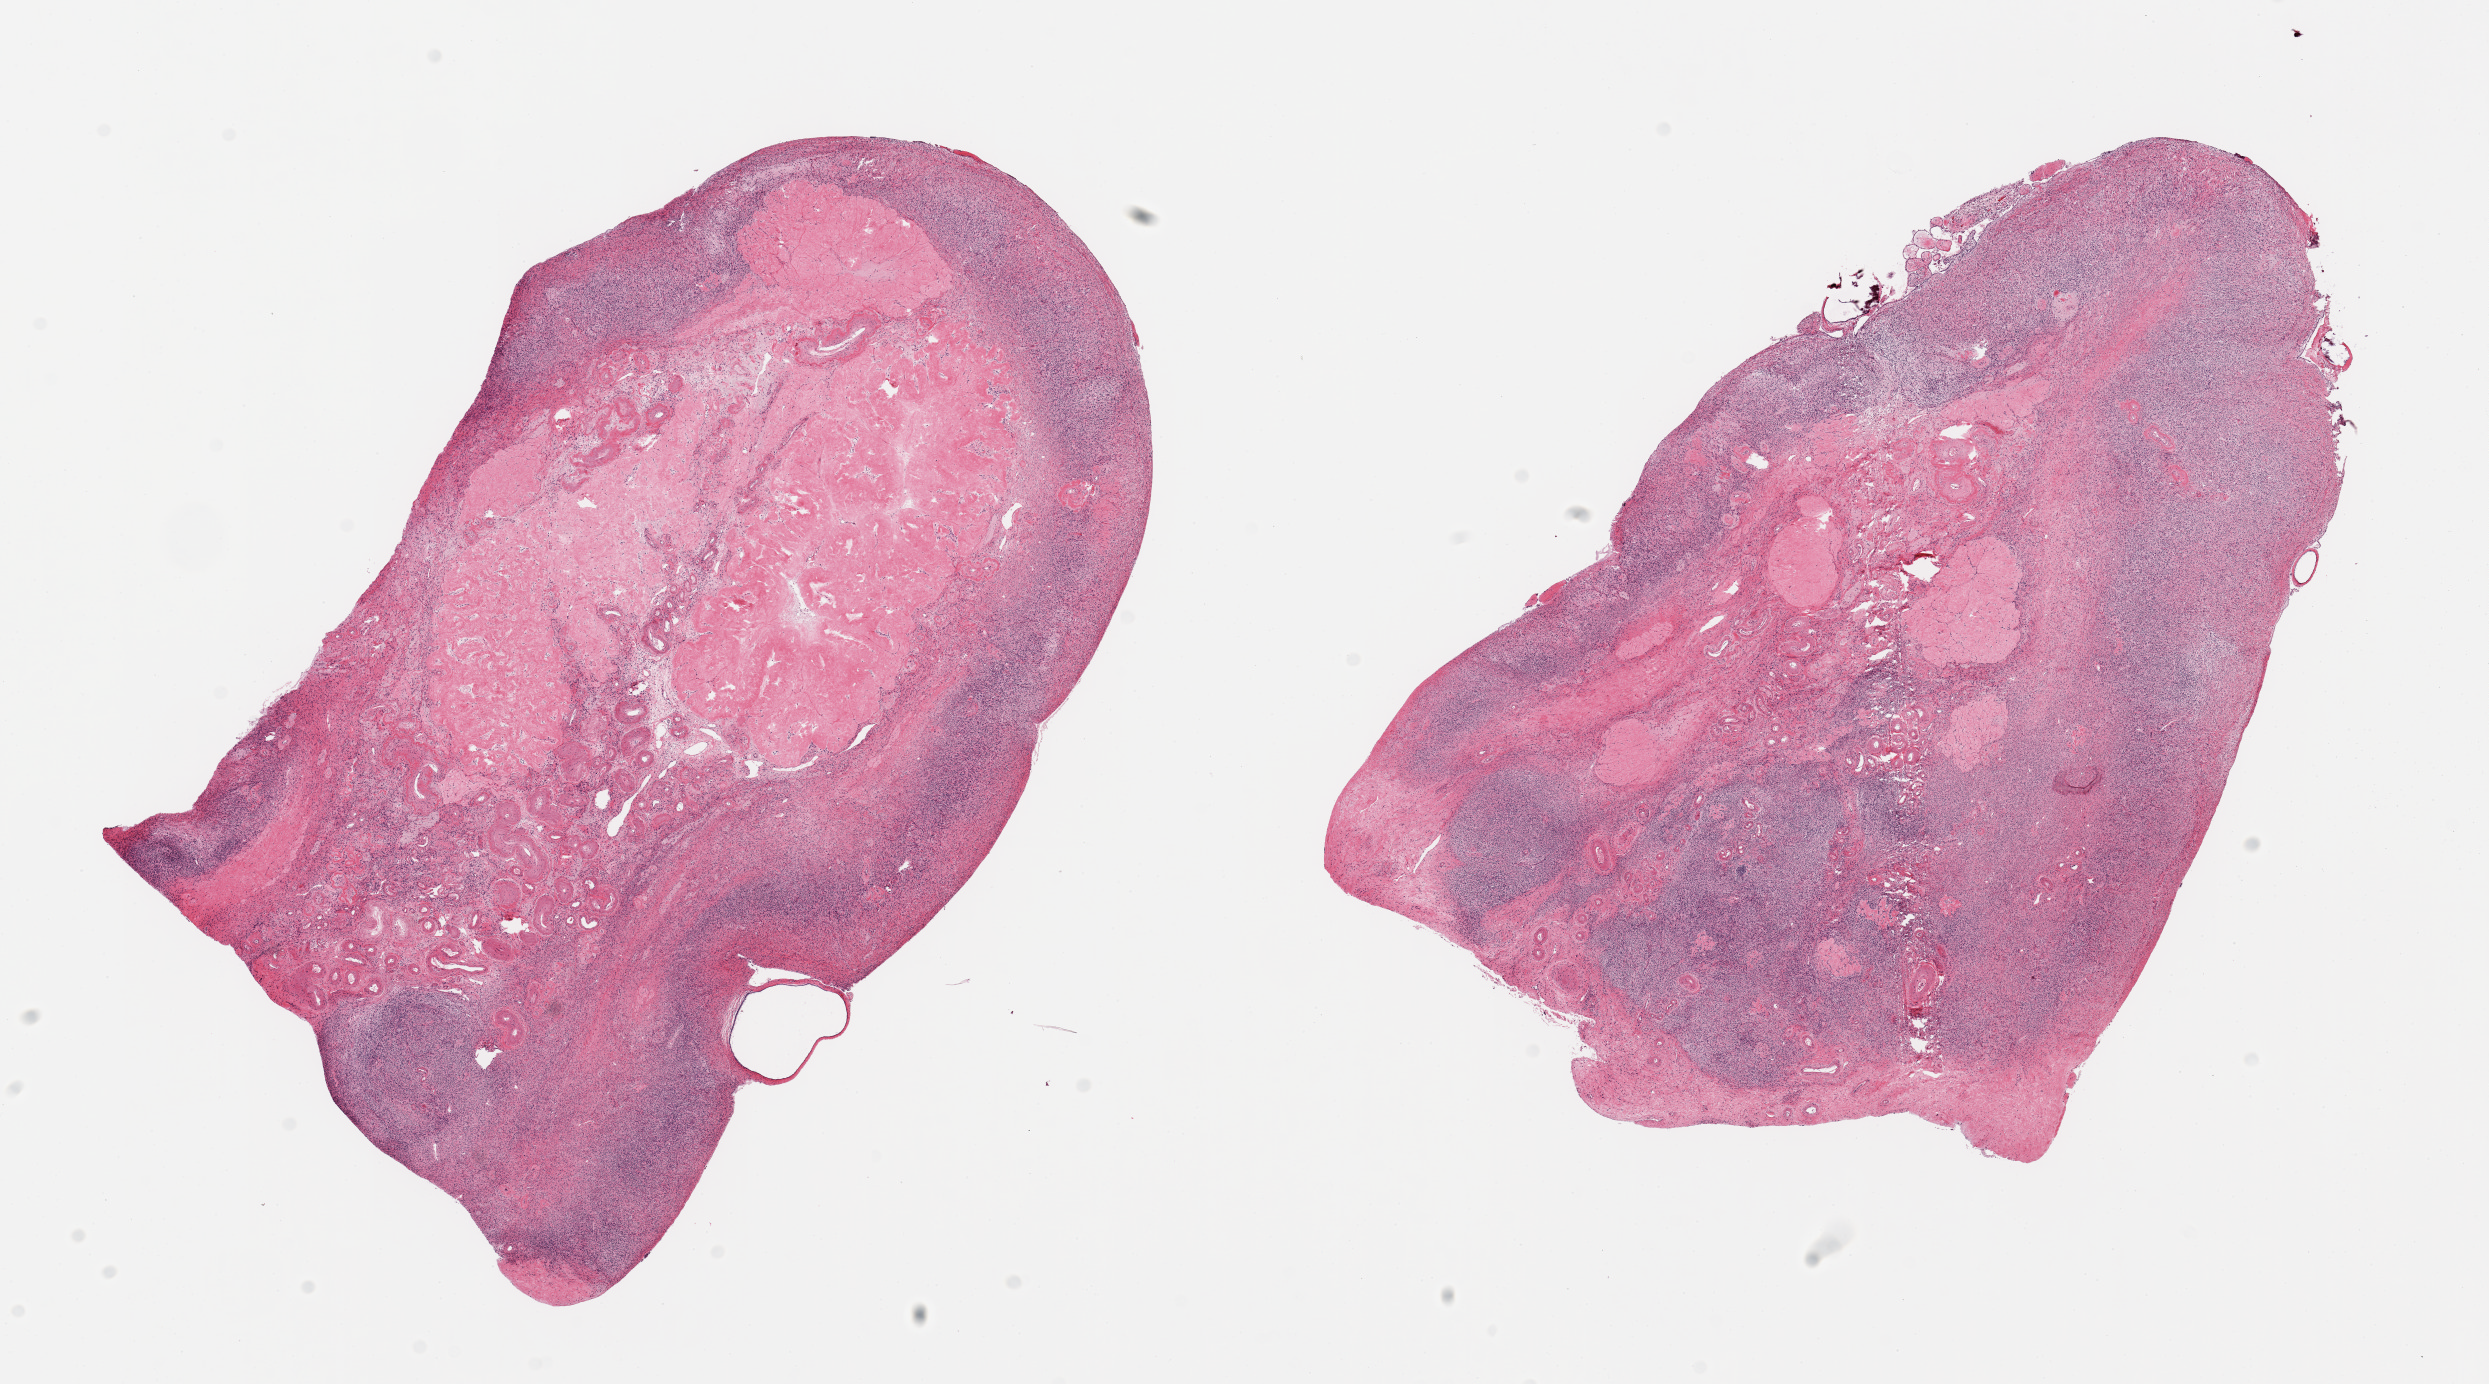
Whole-slide image, haematoxylin and eosin stain, low-resolution overview of the scanned area, about 19.7 x 10.9 mm (slide scanned at 20x); PAXgene-fixed paraffin-embedded (PFPE) section; target tissue: ovary; tissue donor sample.
* review note (as recorded): 2 pieces; postmenopausal involutional changes, epithelial inclusion cysts and papillary stromal projections with calcification